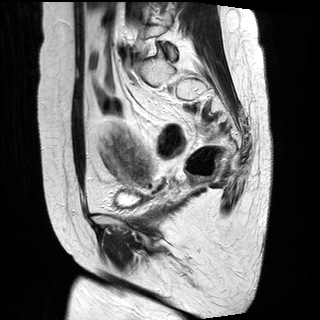
Pelvic MRI for cervical cancer, one sagittal slice; slice 11 of 29 in the series (ordered by position); T2-weighted; 1.5 T; TE 89 ms, TR 2930 ms; 4 mm slice thickness; 320 × 320 image matrix, field of view 260 × 260 mm. Female patient, age 49 years.
Outlined on this slice (expert manual segmentation):
- uterus and cervix: box from (x=101, y=128) to (x=155, y=187) px